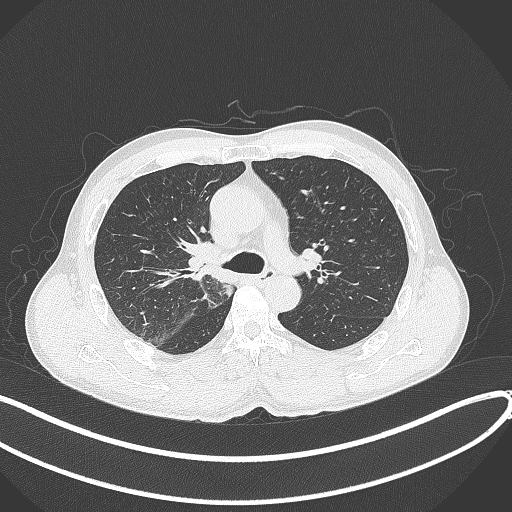
Chest CT, one axial slice. Slice 255 of 409 in the series (ordered by position). Reconstruction kernel B70f. 120 kVp. Lung window (W 1500 / L -600 HU). 512 × 512 image matrix, field of view 400 × 400 mm. Male patient, age 53 years. Case-level facts recorded for this patient, not image findings: clinical TNM (as recorded): T1b N0 M0.
Structures marked on this image (rectangle marked by the reading radiologist):
- lung tumour (recorded histology: squamous cell carcinoma): bounding box (x1, y1, x2, y2) in pixels: (180, 236, 224, 282)